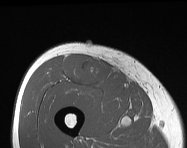
MRI of an extremity soft-tissue mass, one axial slice; position 62 of 114 along the scan axis; MR volume resampled by the dataset authors to the PET/CT grid (not the native acquisition matrix); 3.27 mm slice thickness; 187 × 148 image matrix, field of view 183 × 145 mm. Male patient. Case-level facts recorded for this patient, not image findings: histological type: pleiomorphic leiomyosarcoma; grade: intermediate; site of the primary tumour: right thigh.
Outlined on this slice (expert contour drawn on MRI and transferred to this co-registered scan by the dataset authors):
- gross tumour volume including surrounding oedema: box from (x=64, y=54) to (x=110, y=85) px